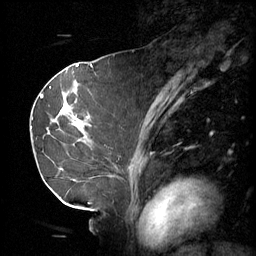
Breast MRI (dynamic contrast-enhanced), one sagittal slice. Position 30 of 60 along the scan axis. 3 images stored at this slice position (order not interpretable as contrast timing). 1.5 T. TE 4.2 ms, TR 11 ms. 2 mm slice thickness. 256 × 256 image matrix, field of view 220 × 220 mm. Patient: female, 69 years.
Annotated regions visible in this slice (semi-automatic segmentation, software-assisted and operator-edited):
- analysis volume of interest (the breast-tissue region the enhancement analysis was run in; not a lesion): box from (x=36, y=88) to (x=96, y=189) px
- tumour enhancement mask (voxels above the 70 % enhancement threshold inside the analysis volume of interest): (x=41, y=88)–(x=87, y=137)